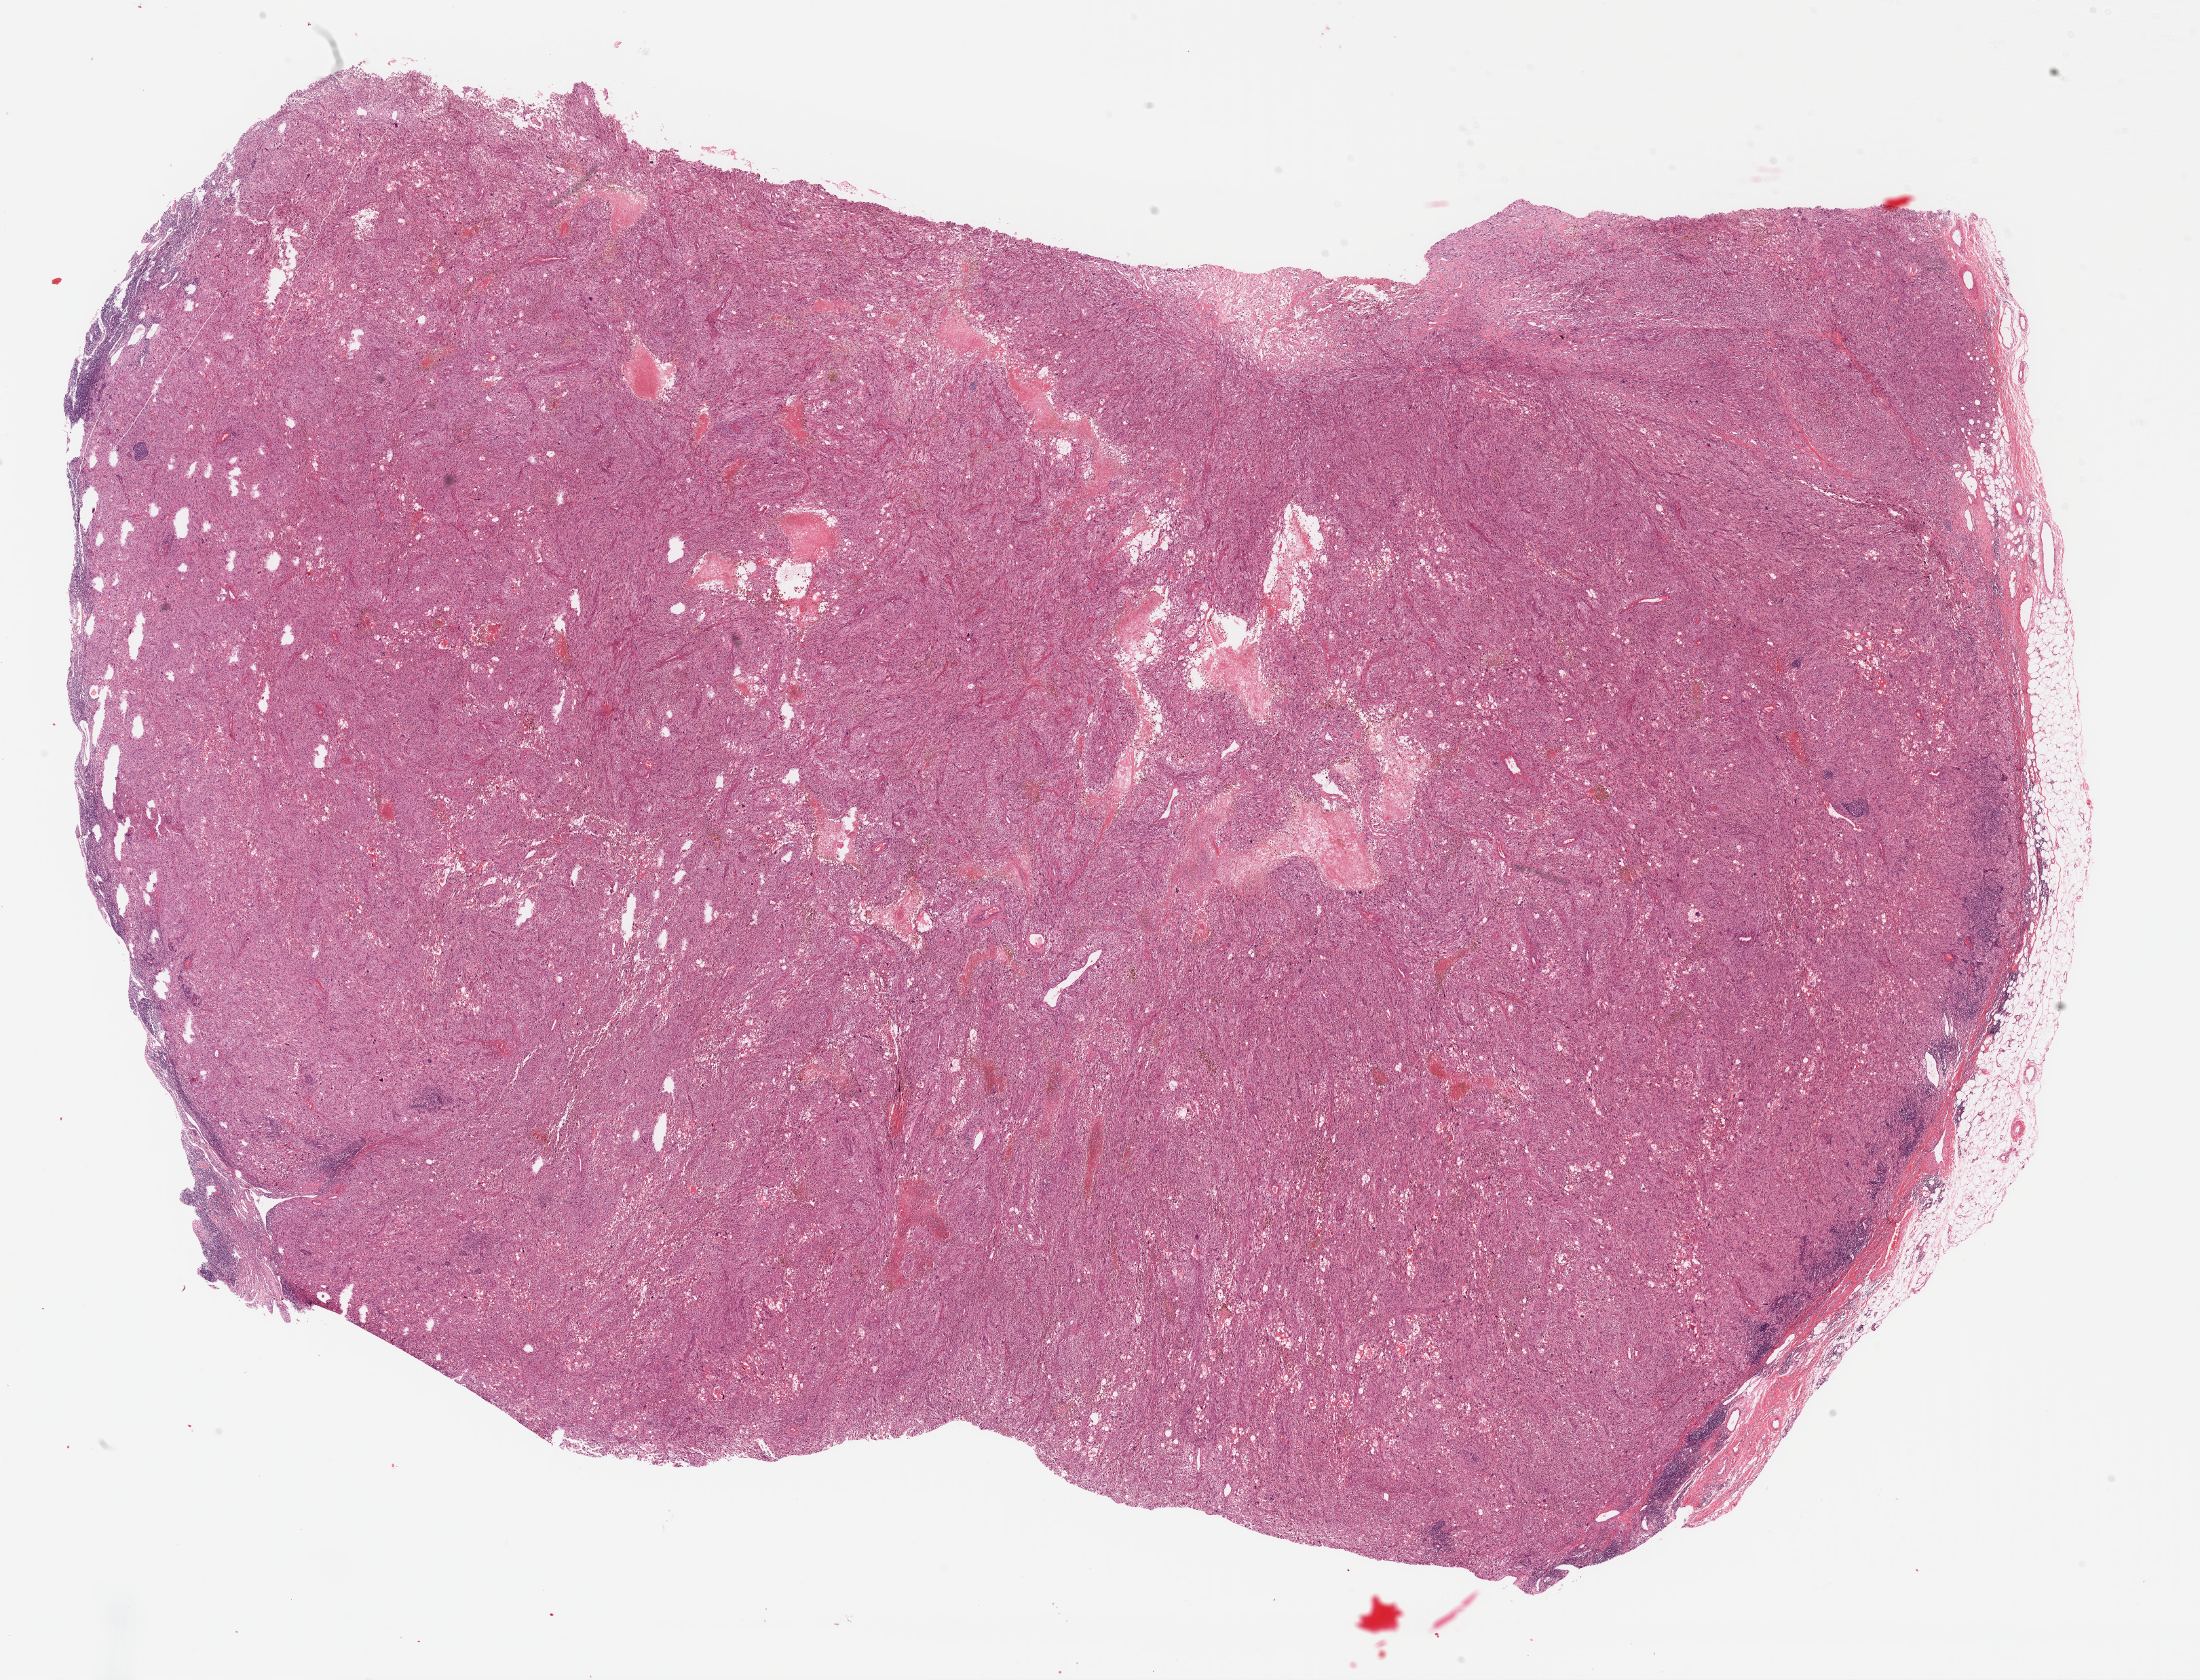
H&E whole-slide image — a low-resolution overview of the entire scanned area, about 25.5 x 19.5 mm. Formalin-fixed paraffin-embedded (FFPE) diagnostic section. Skin, primary tumour sample. Male, age 55 years at initial diagnosis.
* diagnosis: Malignant melanoma, NOS